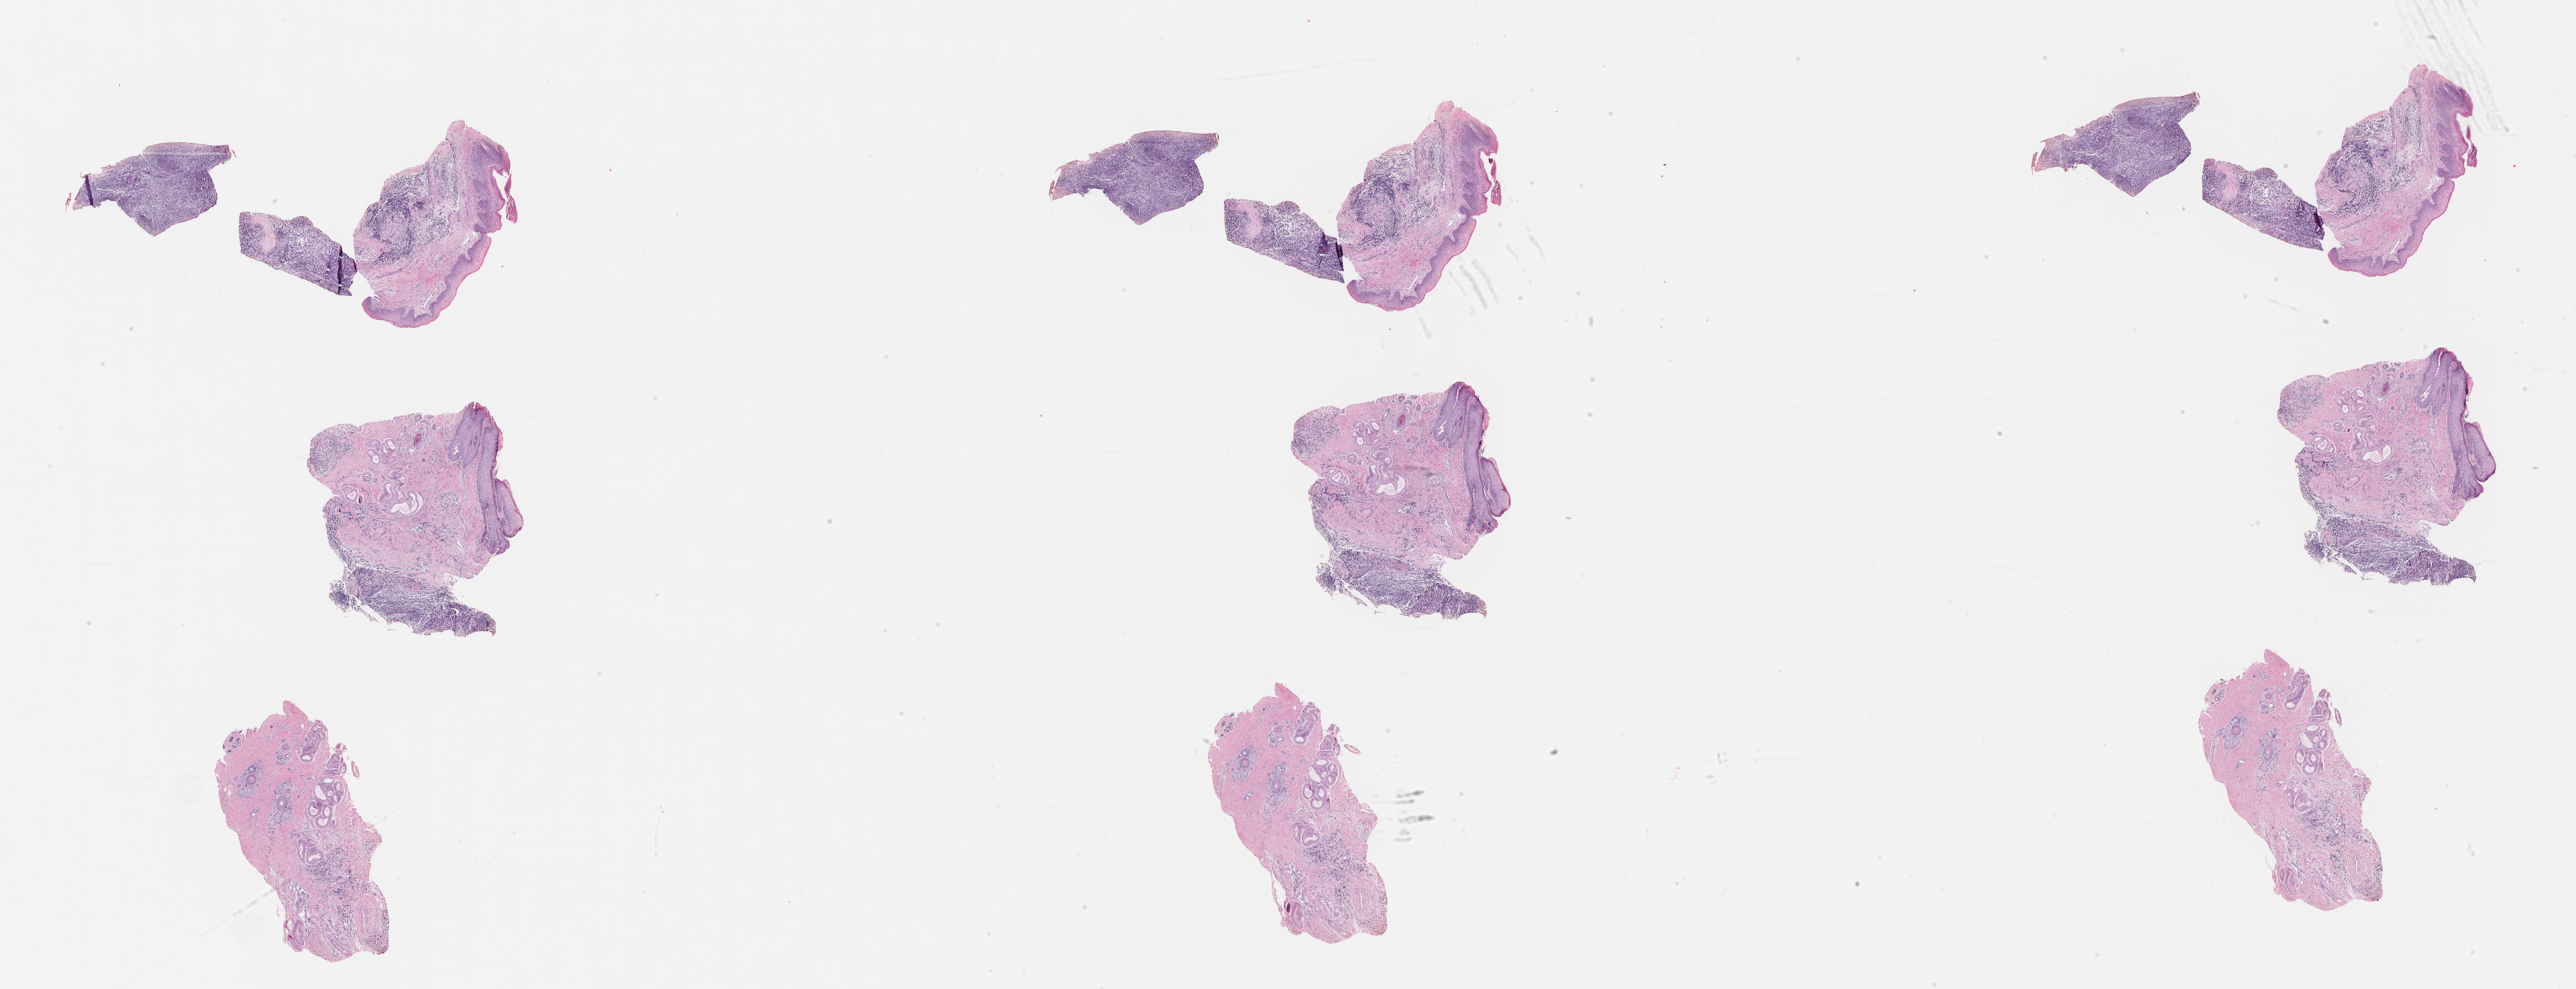
Digitized H&E-stained section of tumor tissue, a low-resolution overview of the entire scanned area, about 30.2 x 11.6 mm; formalin-fixed, paraffin-embedded (FFPE) tissue; site: soft tissue, ear-left. Patient: male, age 4.8 years at diagnosis.
Diagnosis: rhabdomyosarcoma; histological classification: embryonal rhabdomyosarcoma.